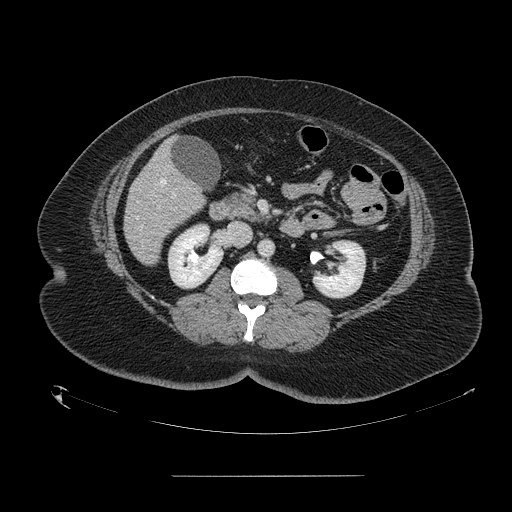
Contrast-enhanced abdominal CT, one axial slice. Slice 59 of 164 in the series (ordered by position). 120 kVp. Intravenous contrast given. Soft-tissue window (W 400 / L 40 HU). 512 × 512 image matrix, field of view 495 × 495 mm. Female patient, age 52 years. From the clinical record (not read from this slice): diagnosis: colorectal cancer liver metastases, imaged before liver resection; multiple liver metastases: yes; largest metastasis: 3.5 cm.
Annotated regions visible in this slice (outlined manually by an expert reader):
- hepatic veins: bounding box (x1, y1, x2, y2) in pixels: (136, 179, 166, 230)
- liver: (124, 143, 205, 265)
- portal vein (with intrahepatic branches): (171, 193, 175, 197)